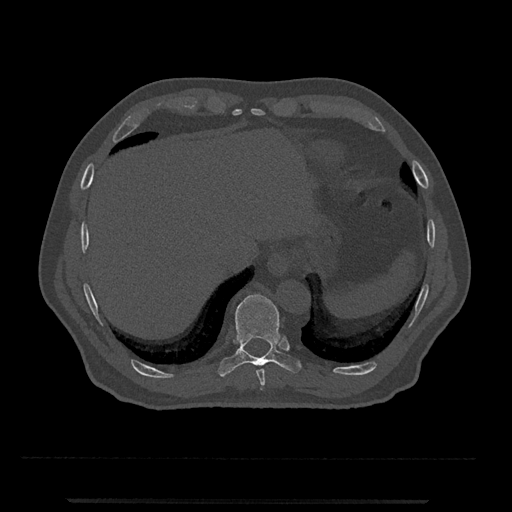
CT including the spine, one axial slice. Position 529 of 797 along the scan axis. Reconstruction kernel Br40s/3. 120 kVp. Bone window (W 1800 / L 400 HU). 0.5 mm slice thickness. 512 × 512 image matrix, field of view 419 × 419 mm. Patient: male, 63 years. Case-level facts recorded for this patient, not image findings: primary cancer: prostate.
Outlined on this slice (semi-automatically segmented with operator editing):
- T10 vertebra: box from (x=218, y=294) to (x=302, y=377) px
- T9 vertebra: (x=256, y=369)–(x=265, y=390)